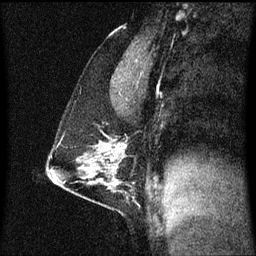
Breast MRI (dynamic contrast-enhanced), one sagittal slice; position 36 of 60 along the scan axis; dynamic contrast-enhanced series, image 2 of 3 at this slice position (ordered by acquisition); 1.5 T; TE 4.2 ms, TR 8.4 ms; 2 mm slice thickness; 256 × 256 image matrix, field of view 200 × 200 mm. Patient: female, 40 years. From the clinical record (not read from this slice): setting: breast cancer imaged before/during neoadjuvant chemotherapy; receptor status: triple-negative.
Outlined on this slice (semi-automatically segmented with operator editing):
- analysis volume of interest (the breast-tissue region the enhancement analysis was run in; not a lesion): bounding box <48,132,129,195> (left, top, right, bottom; pixels)
- tumour enhancement mask (voxels above the 70 % enhancement threshold inside the analysis volume of interest): <117,146,126,149>